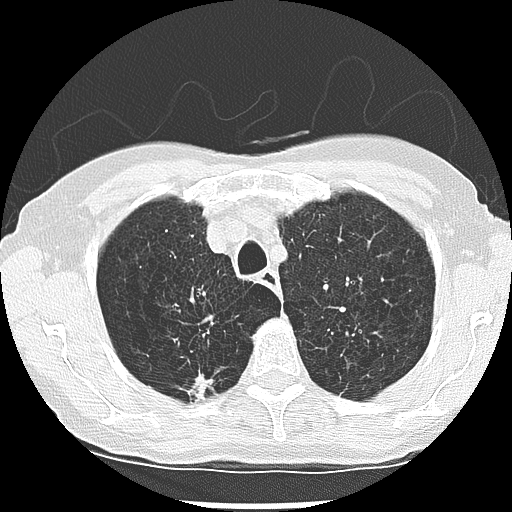
Low-dose screening chest CT, one axial slice; position 220 of 265 along the scan axis; 120 kVp; lung window (W 1500 / L -600 HU); 512 × 512 image matrix, field of view 300 × 300 mm.
Annotated regions visible in this slice (expert manual segmentation):
- lesion 1 (nodule, upper lobe of right lung): bounding box (x1, y1, x2, y2) in pixels: (188, 374, 213, 399)